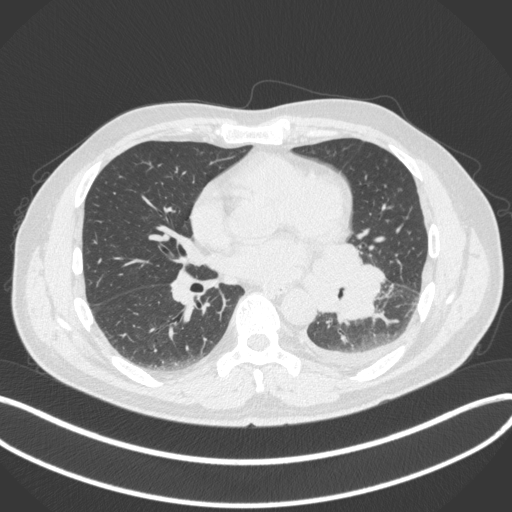
Chest CT, one axial slice. Position 169 of 350 along the scan axis. Reconstruction kernel B31f. Lung window (W 1500 / L -600 HU). 1 mm slice thickness. 512 × 512 image matrix, field of view 400 × 400 mm. Male patient, age 58 years. From the clinical record (not read from this slice): clinical TNM (as recorded): T3 N1 M1b.
Annotated regions visible in this slice (bounding box drawn by a radiologist):
- lung tumour (recorded histology: small cell carcinoma): bounding box <308,246,387,320> (left, top, right, bottom; pixels)